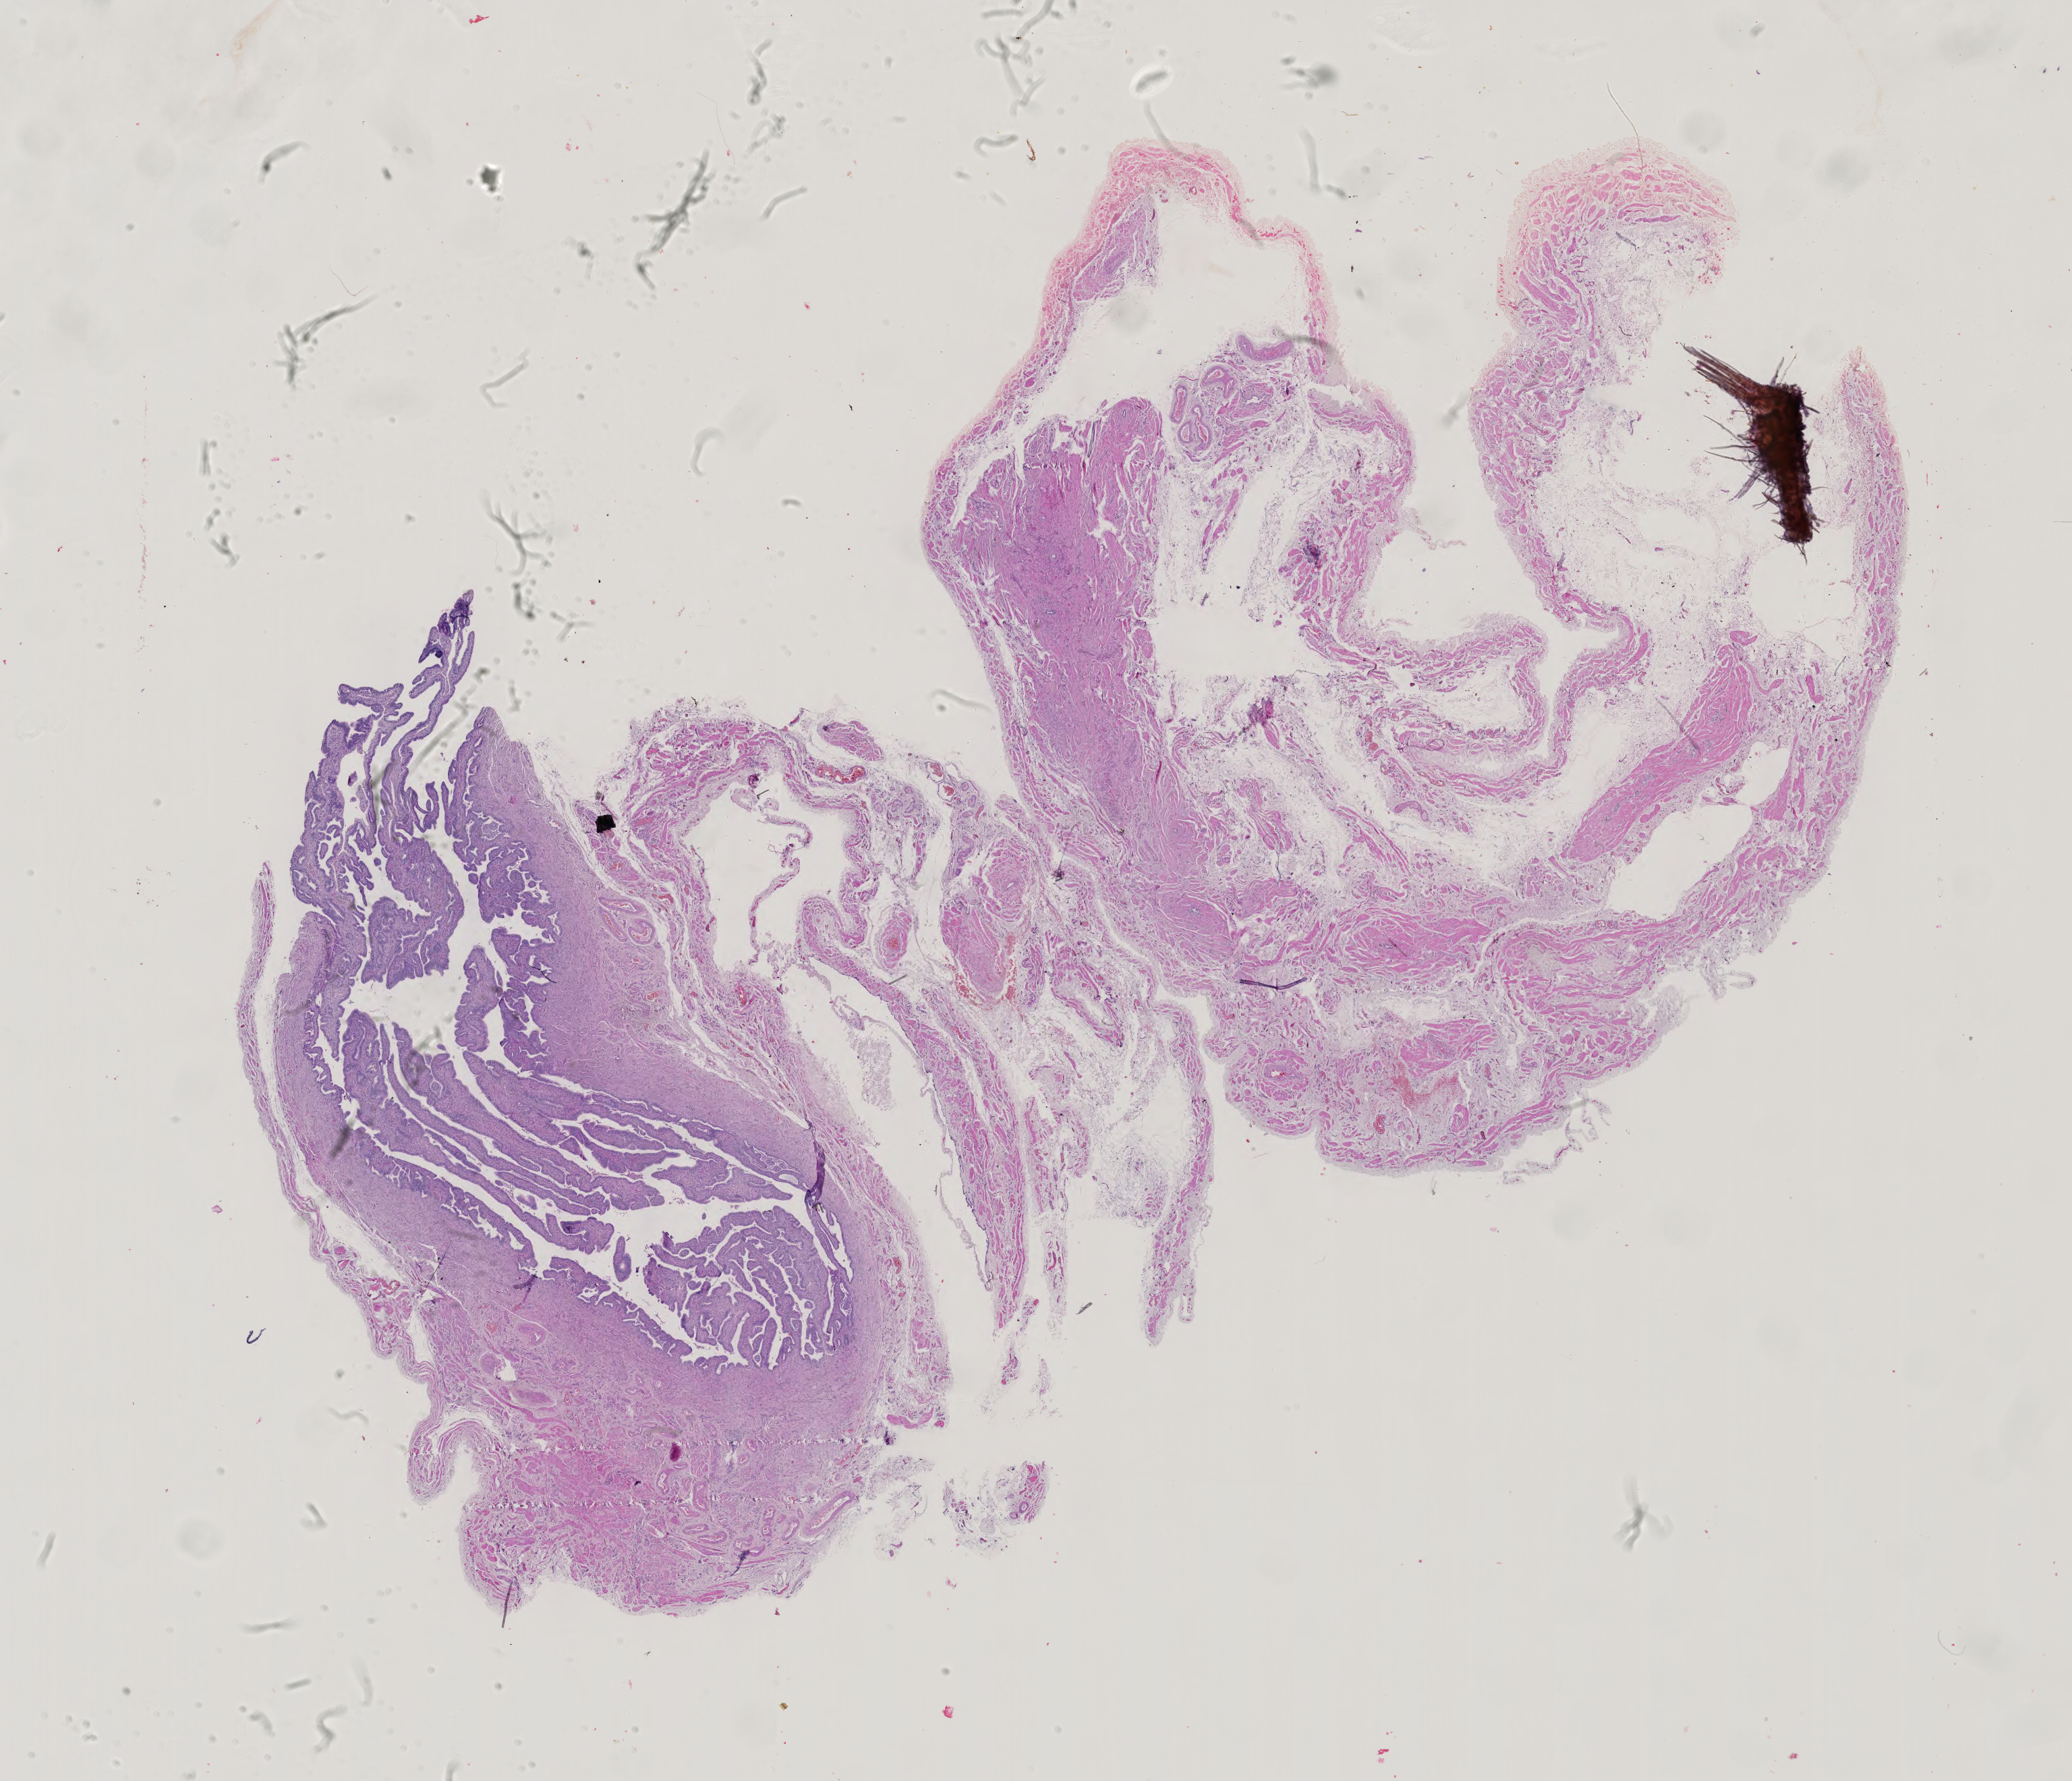
Hematoxylin and eosin (H&E) stained whole-slide image — a low-resolution overview of the entire scanned area, about 22.4 x 19.2 mm (from a 40x scan); formalin-fixed paraffin-embedded (FFPE) diagnostic section; testis, primary tumour sample. Male patient; age at initial diagnosis 26 years.
- AJCC pathologic stage: II (4th edition)
- diagnosis: Embryonal carcinoma, NOS